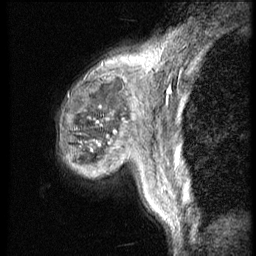
Breast MRI (dynamic contrast-enhanced), one sagittal slice; position 12 of 56 along the scan axis; 4 images stored at this slice position (order not interpretable as contrast timing); 1.5 T; TE 4.2 ms, TR 9 ms; 2.5 mm slice thickness; 256 × 256 image matrix. Patient: female, 50 years. From the clinical record (not read from this slice): setting: breast cancer imaged before/during neoadjuvant chemotherapy; receptor status: triple-negative.
Structures marked on this image (semi-automatically segmented with operator editing):
- analysis volume of interest (the breast-tissue region the enhancement analysis was run in; not a lesion): bounding box <55,52,148,188> (left, top, right, bottom; pixels)
- tumour enhancement mask (voxels above the 140 % enhancement threshold inside the analysis volume of interest): <114,56,132,134>